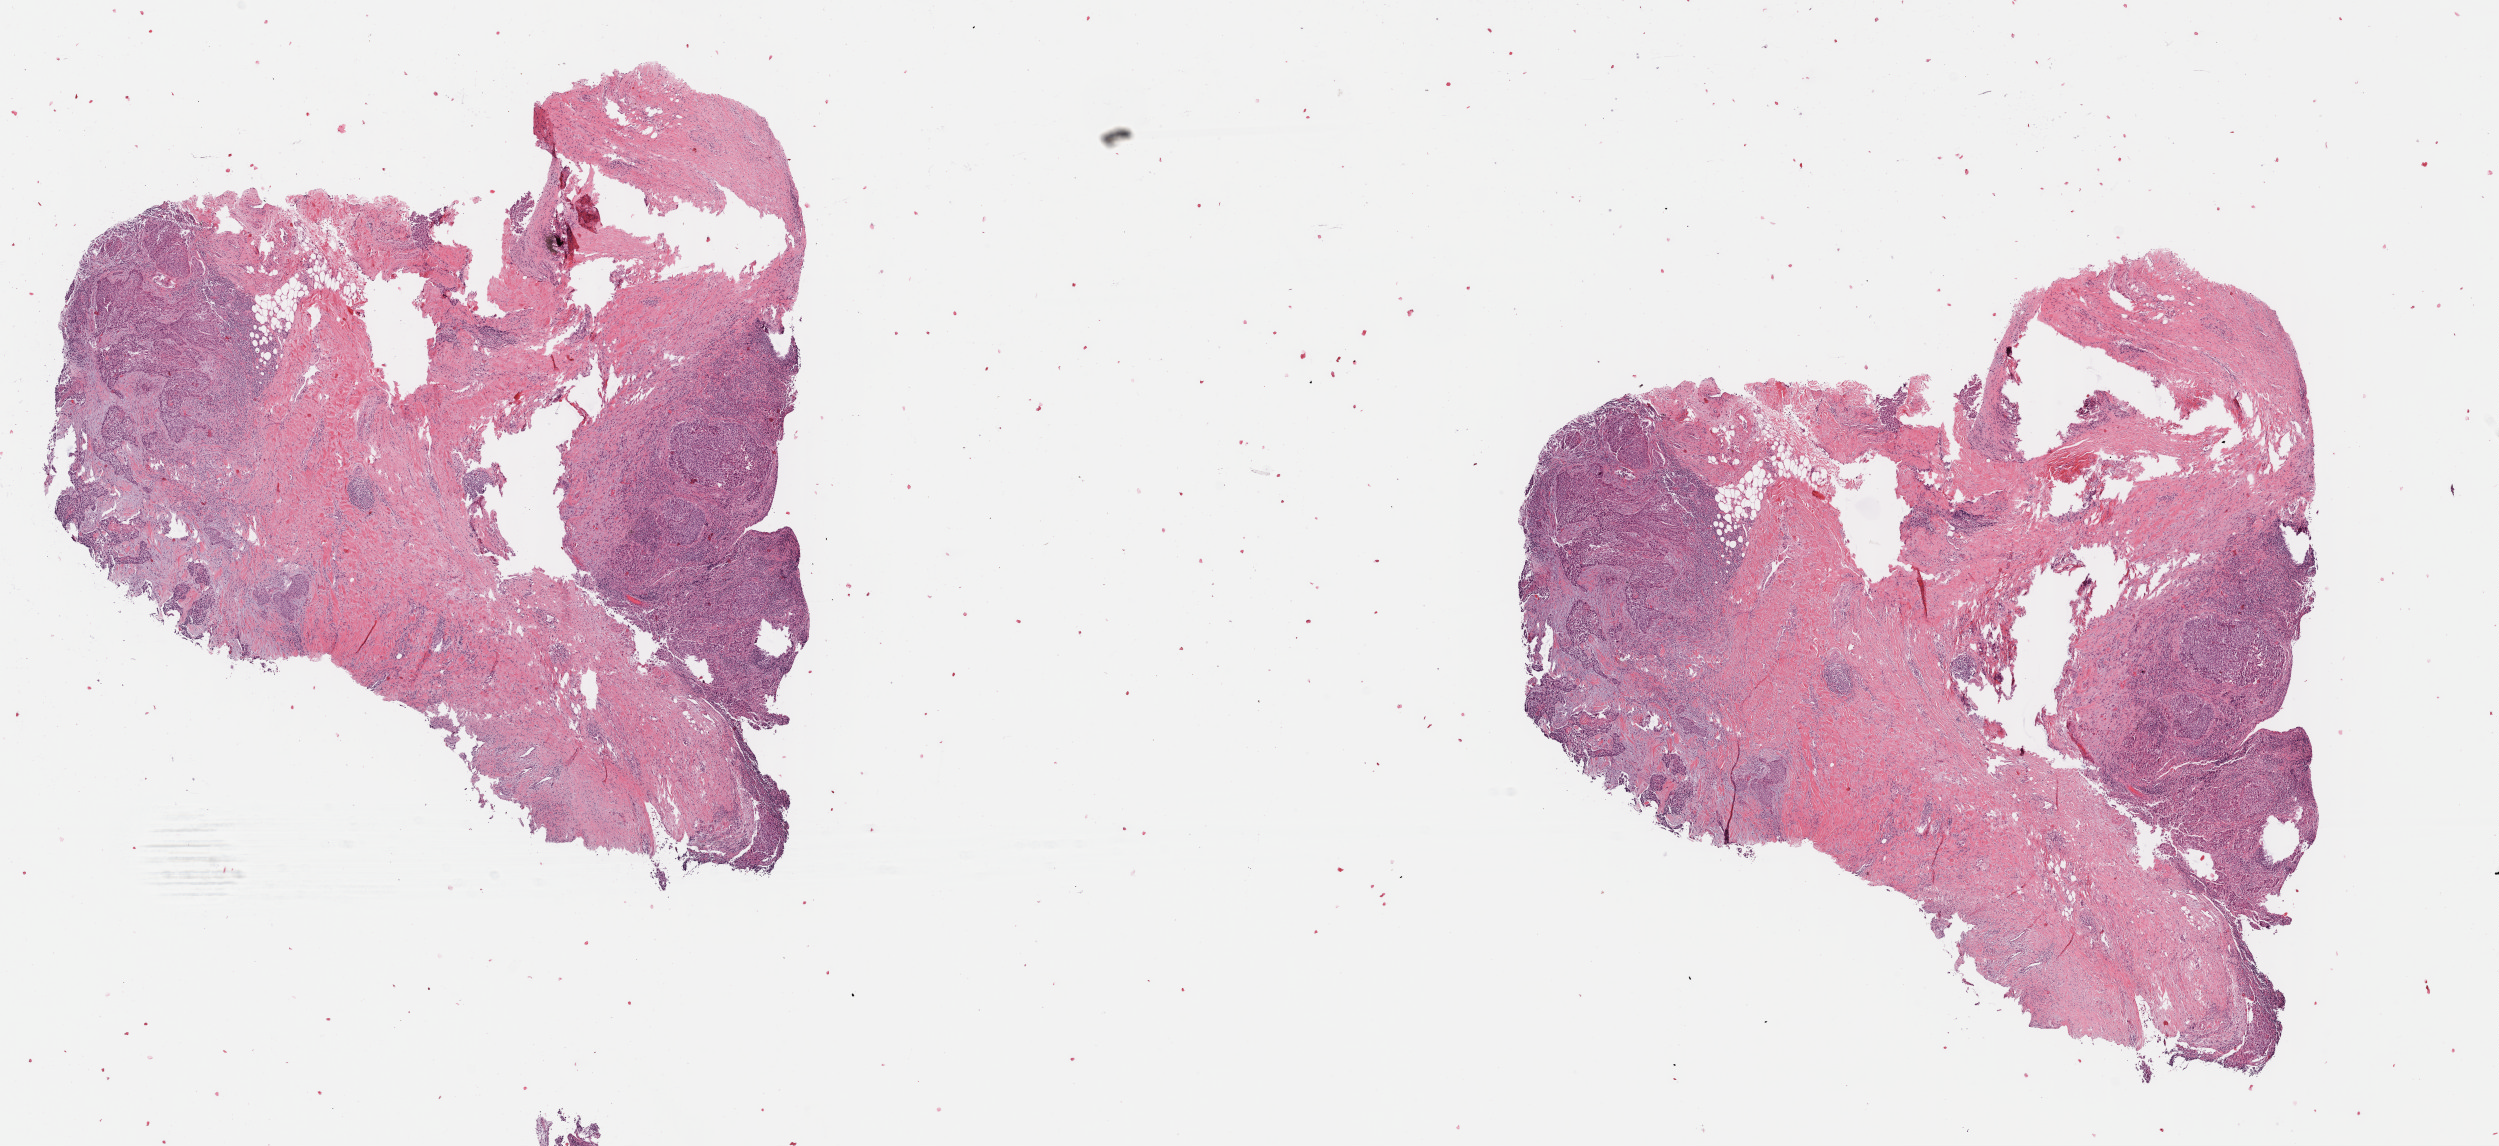
Digitized H&E tissue section (whole slide), low-resolution overview of the scanned area, about 19.6 x 9.0 mm (acquisition: 40x scan); FFPE section; primary tumour sample from the lung. Male, age 64 years at initial diagnosis.
Histologic diagnosis: Squamous cell carcinoma, NOS (upper lobe, lung).